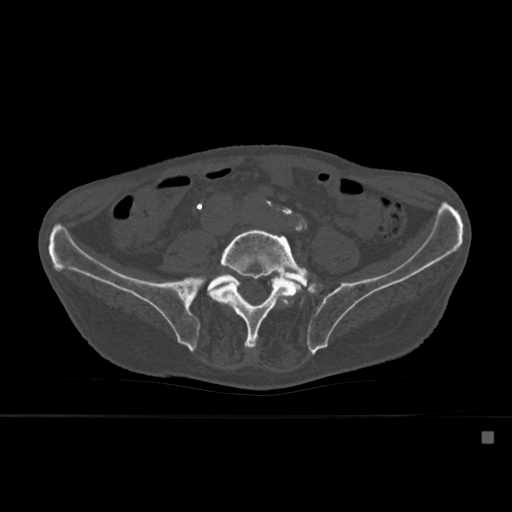
CT including the spine, one axial slice; position 176 of 527 along the scan axis; bone window (W 1800 / L 400 HU); 1.5 mm slice thickness; 512 × 512 image matrix, field of view 373 × 373 mm. Male patient, age 78 years. Case-level facts recorded for this patient, not image findings: primary cancer: prostate.
Outlined on this slice (semi-automatically segmented with operator editing):
- L4 vertebra: bounding box <221,296,292,307> (left, top, right, bottom; pixels)
- L5 vertebra: <209,228,316,348>